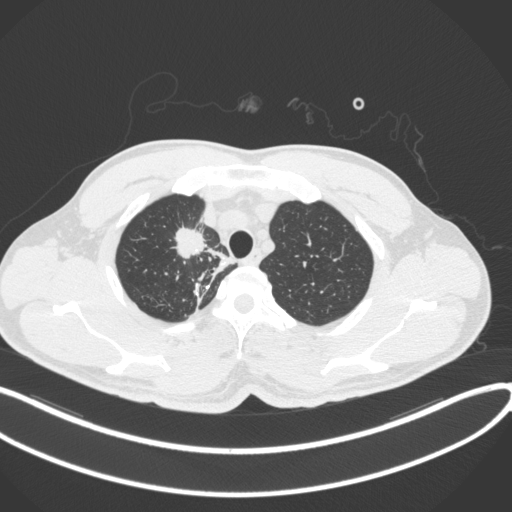
Chest CT, one axial slice; reconstruction kernel B31f; lung window (W 1500 / L -600 HU); 1 mm slice thickness; 512 × 512 image matrix, field of view 400 × 400 mm. Patient: male, 48 years. Case-level facts recorded for this patient, not image findings: clinical TNM (as recorded): T1c N1 M1.
Outlined on this slice (rectangle marked by the reading radiologist):
- lung tumour (recorded histology: adenocarcinoma): box from (x=168, y=227) to (x=209, y=261) px